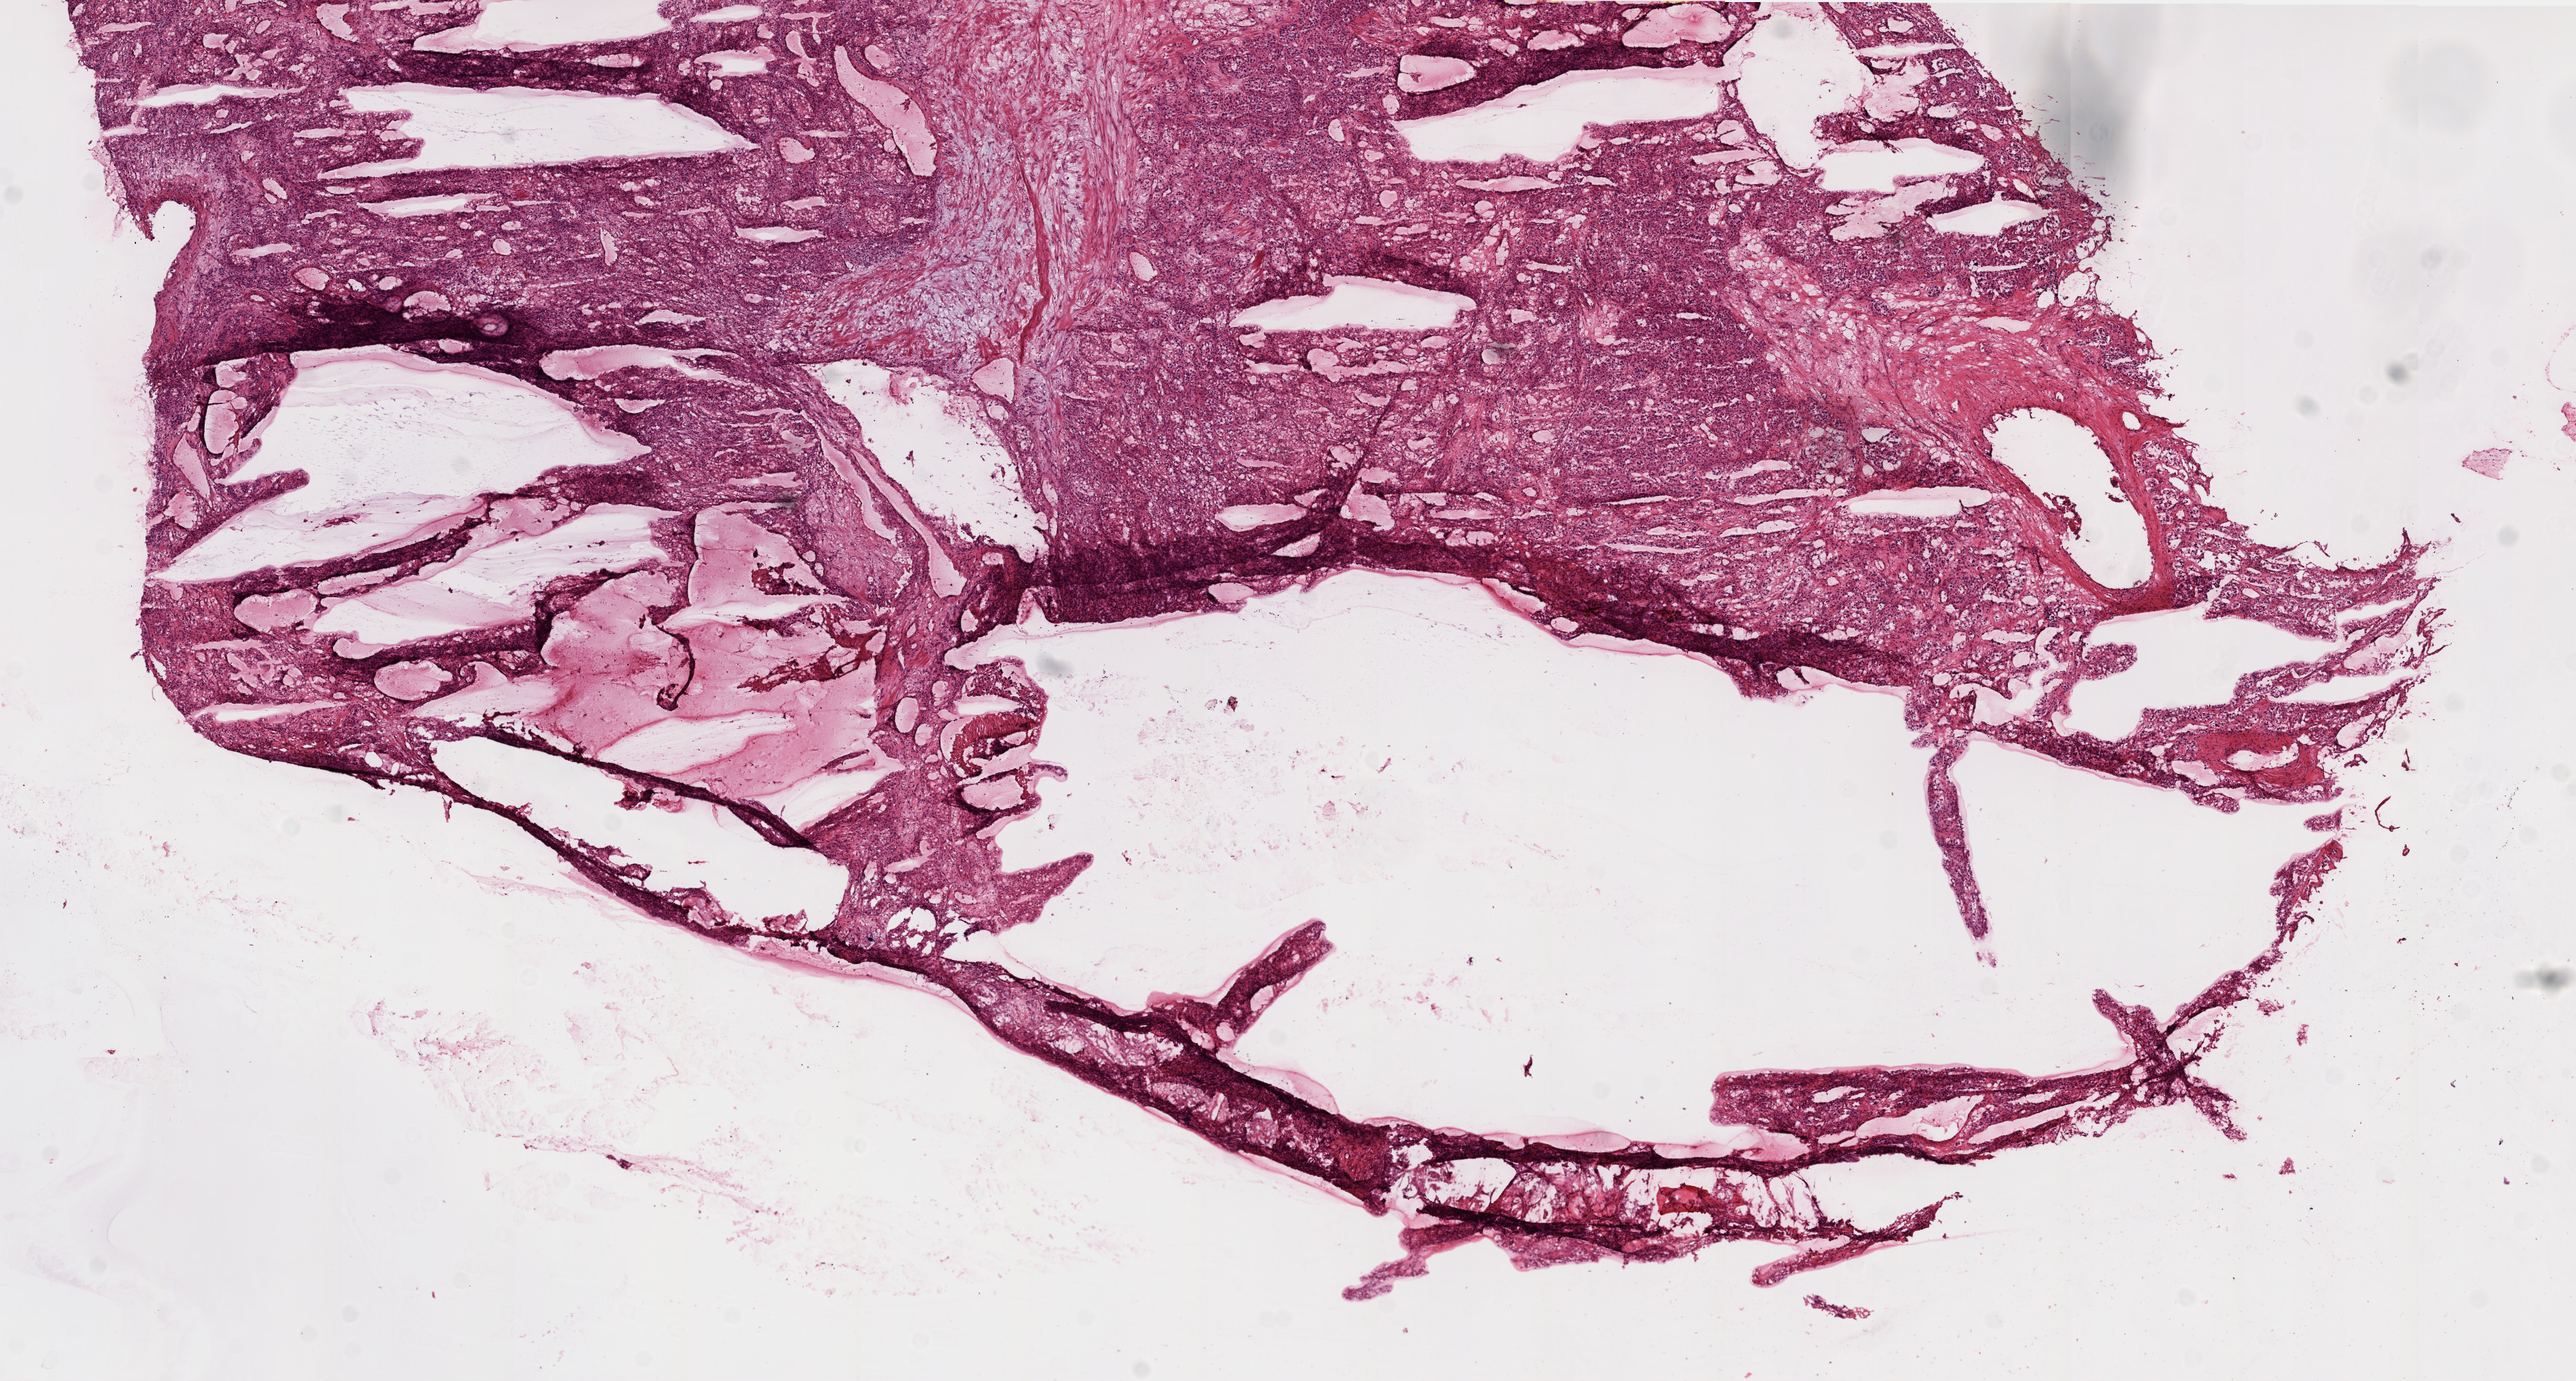
H&E-stained whole-slide image, low-resolution overview of the scanned area, about 15.0 x 8.1 mm. Frozen section from the top of the tissue portion. Primary tumour sample from the kidney. Male patient; age at initial diagnosis 57 years. Composition of this section per pathologist review: tumour cells 90%, tumour nuclei 90%.
Pathologic diagnosis: Clear cell adenocarcinoma, NOS.